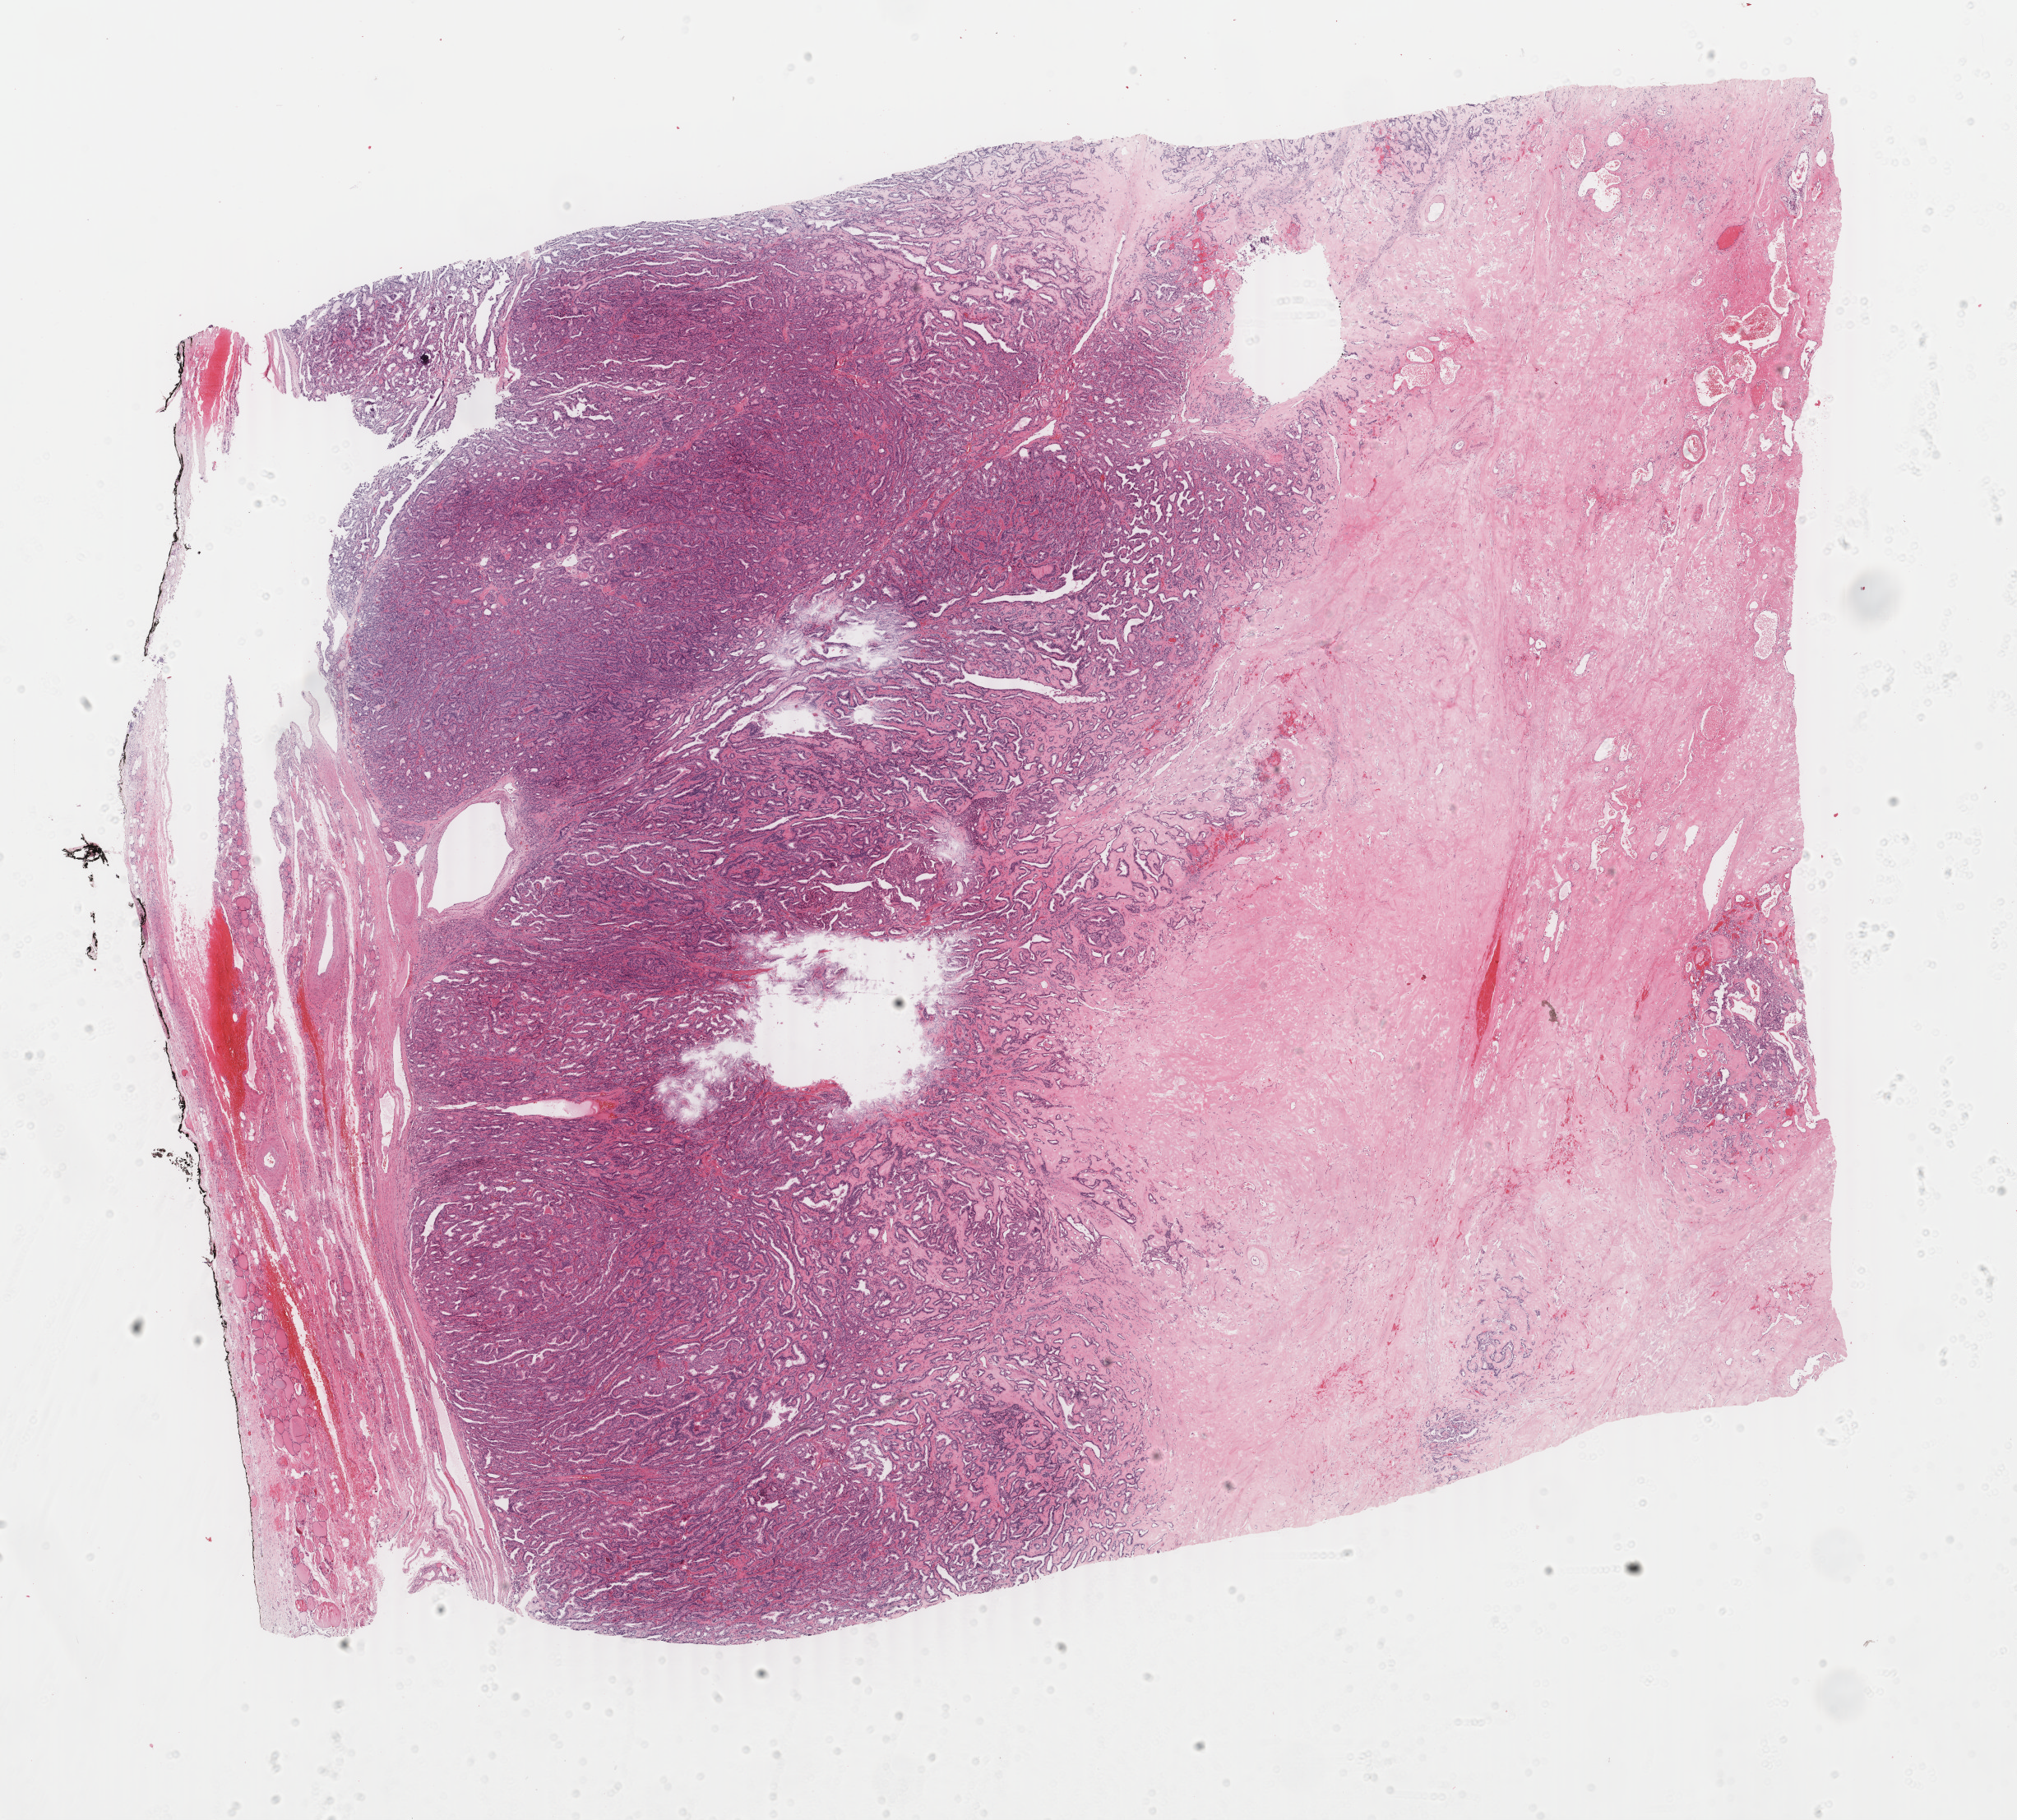
Digitized H&E-stained tissue section (whole slide), a low-resolution overview of the entire scanned area, about 19.5 x 17.6 mm (slide scanned at 40x); formalin-fixed paraffin-embedded (FFPE) diagnostic section; thyroid, primary tumour sample. Male, age 82 years at initial diagnosis.
AJCC pathologic stage: III (6th edition). Histologic diagnosis: Papillary adenocarcinoma, NOS. Lymph nodes positive (case pathology): 0 of 2 examined.